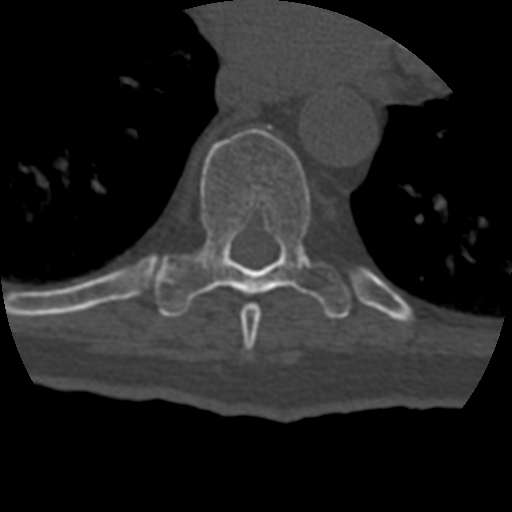
CT including the spine, one axial slice. Position 243 of 399 along the scan axis. 120 kVp. Bone window (W 1800 / L 400 HU). 512 × 512 image matrix, field of view 160 × 160 mm. Patient age 69 years. Case-level facts recorded for this patient, not image findings: primary cancer: prostate.
Annotated regions visible in this slice (semi-automatically segmented with operator editing):
- T8 vertebra: box from (x=241, y=303) to (x=262, y=350) px
- T9 vertebra: (x=152, y=128)–(x=351, y=319)